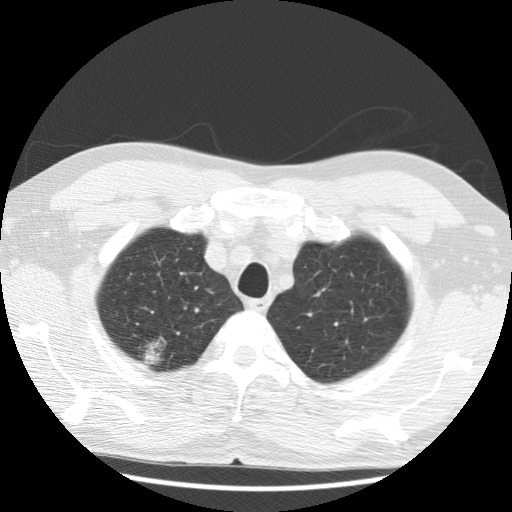
Low-dose screening chest CT, axial slice; first (baseline) screen; lung window (W 1500 / L -600 HU); 120 kVp; slice 21 of 122 in the series; 512 × 512 image matrix. Male, age 59 years at enrolment.
Expert-annotated lung lesion, bounding box [x1, y1, x2, y2] px = [128, 329, 182, 381]. Reader record for this screening exam (exam-level; its link to the box is not recorded): non-calcified nodule or mass ≥4 mm, right upper lobe, 30 × 28 mm, poorly defined margins, ground glass attenuation.